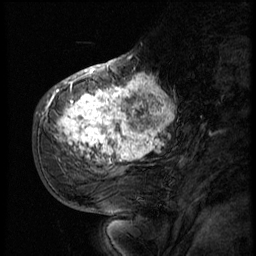
Breast MRI (dynamic contrast-enhanced), one sagittal slice. Slice 22 of 56 in the series (ordered by position). 3 images stored at this slice position (order not interpretable as contrast timing). 1.5 T. TE 4.2 ms, TR 9 ms. 2.5 mm slice thickness. 256 × 256 image matrix. Patient: female, 51 years. Case-level facts recorded for this patient, not image findings: setting: breast cancer imaged before/during neoadjuvant chemotherapy; receptor status: triple-negative.
Structures marked on this image (semi-automatic segmentation, software-assisted and operator-edited):
- analysis volume of interest (the breast-tissue region the enhancement analysis was run in; not a lesion): bounding box <52,66,183,179> (left, top, right, bottom; pixels)
- tumour enhancement mask (voxels above the 140 % enhancement threshold inside the analysis volume of interest): <54,70,175,163>